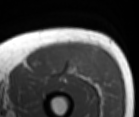
MRI of an extremity soft-tissue mass, one axial slice; position 40 of 86 along the scan axis; MR volume resampled by the dataset authors to the PET/CT grid (not the native acquisition matrix); 3.27 mm slice thickness; 139 × 117 image matrix, field of view 136 × 114 mm. Male patient. From the clinical record (not read from this slice): histological type: extraskeletal osteosarcoma; grade: high; site of the primary tumour: thigh.
Annotated regions visible in this slice (expert contour drawn on MRI and transferred to this co-registered scan by the dataset authors):
- gross tumour volume (mass): bounding box [x1, y1, x2, y2] px = [61, 46, 89, 76]